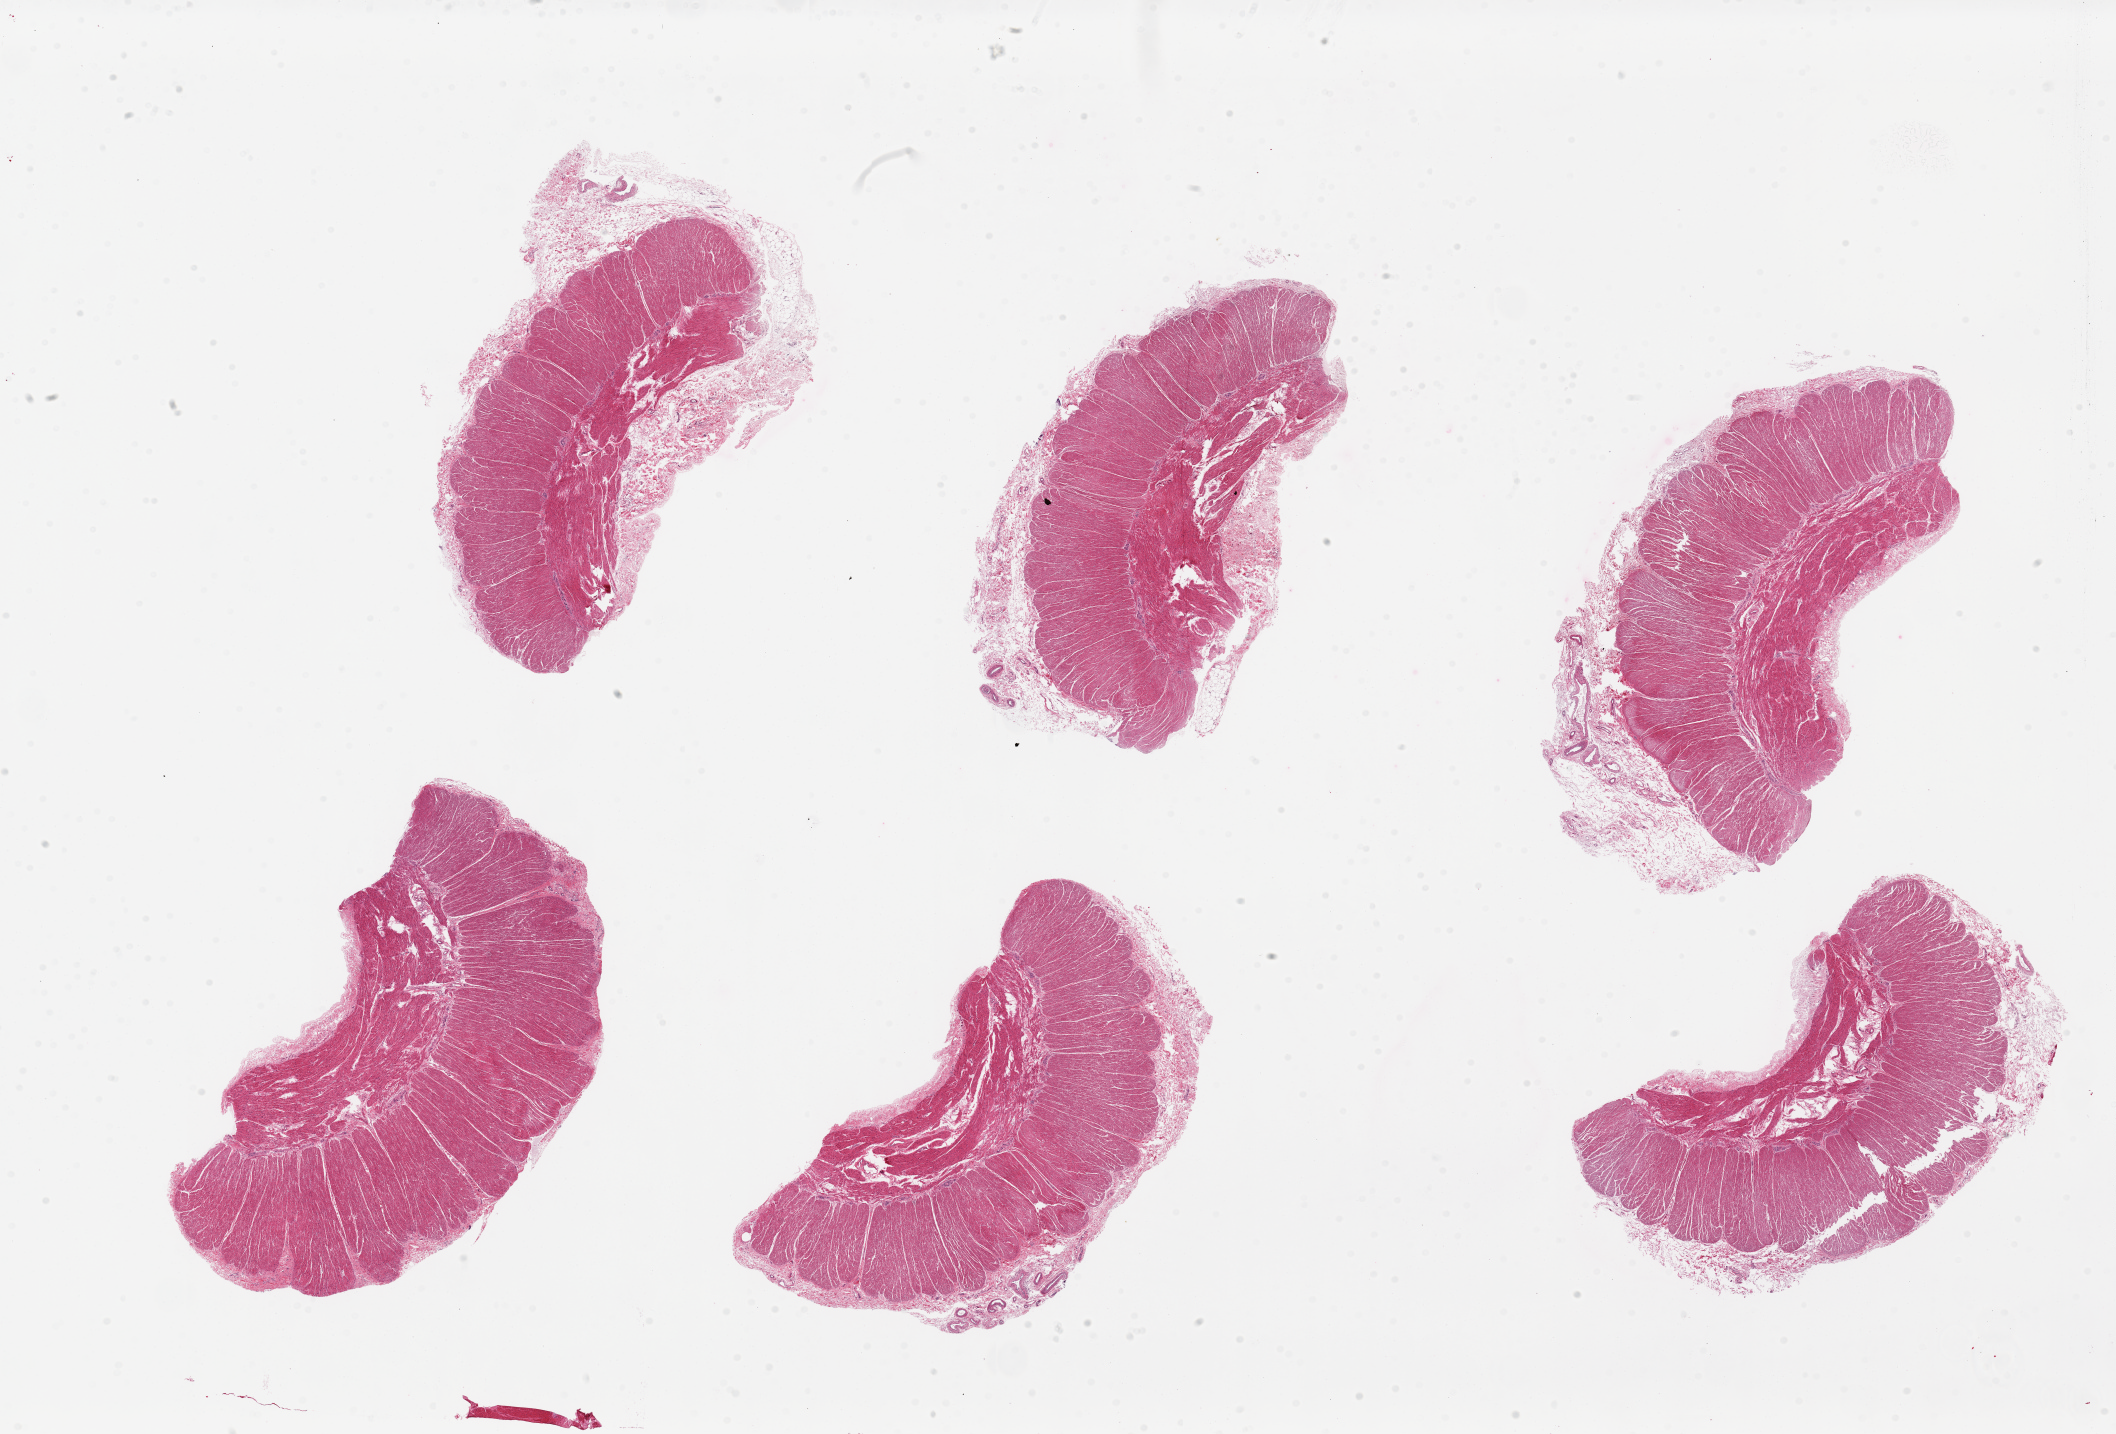
H&E whole-slide image, low-resolution overview of the scanned area, about 33.5 x 22.7 mm (slide scanned at 20x); PAXgene-fixed, paraffin-embedded tissue; target tissue: sigmoid colon; tissue donor sample. Donor sex: male.
Pathologist's review note for this sample: 6 pieces, up to 9x5mm; mainly muscularis, adherent fatty nubbins on 5/6 up to 2 mm in d.